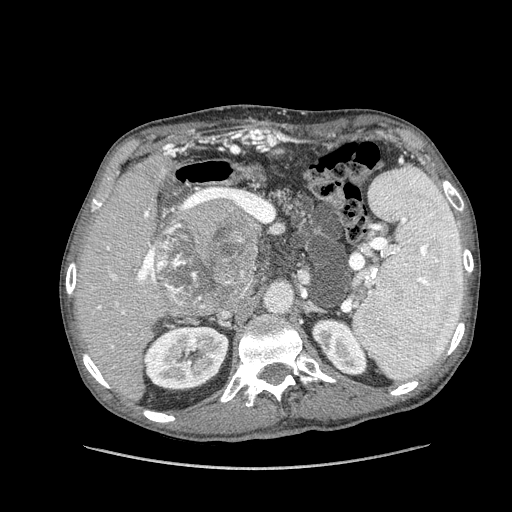
Contrast-enhanced abdominal CT (liver protocol), one axial slice; position 77 of 162 along the scan axis; reconstruction kernel STANDARD; soft-tissue window (W 400 / L 40 HU); 512 × 512 image matrix, field of view 400 × 400 mm. Case-level facts recorded for this patient, not image findings: diagnosis: hepatocellular carcinoma (patient treated with transarterial chemoembolisation; whether this scan precedes or follows treatment is not stated here); TNM stage (as recorded): Stage-IIIA; Child-Pugh class: A; tumour size: 9.9 cm.
Structures marked on this image (semi-automatically segmented with operator editing):
- liver parenchyma outside the tumour (the mass and vessels are separate outlines, so this box may not span the whole liver): bounding box (x1, y1, x2, y2) in pixels: (76, 152, 261, 400)
- mass: (153, 199, 259, 312)
- liver vessels: (97, 211, 155, 348)